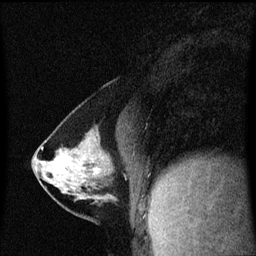
Breast MRI (dynamic contrast-enhanced), one sagittal slice; dynamic contrast-enhanced series, image 2 of 3 at this slice position (ordered by acquisition); 1.5 T; TE 4.2 ms, TR 8.4 ms; 256 × 256 image matrix, field of view 200 × 200 mm. Patient: female, 40 years. From the clinical record (not read from this slice): setting: breast cancer imaged before/during neoadjuvant chemotherapy; receptor status: triple-negative.
Annotated regions visible in this slice (semi-automatically segmented with operator editing):
- analysis volume of interest (the breast-tissue region the enhancement analysis was run in; not a lesion): bounding box [x1, y1, x2, y2] px = [34, 142, 116, 199]
- tumour enhancement mask (voxels above the 70 % enhancement threshold inside the analysis volume of interest): [55, 154, 99, 171]